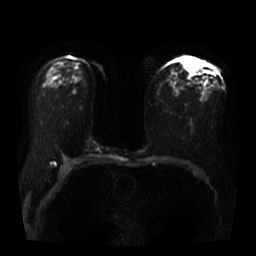
Breast MRI, one axial slice; slice 22 of 40 in the series (ordered by position); diffusion-weighted series; image 2 of 4 stored at this slice position (different b-values; order by instance number); 3 T; 5 mm slice thickness; 256 × 256 image matrix, field of view 360 × 360 mm. Female patient.
Outlined on this slice (expert manual segmentation):
- tumour on diffusion-weighted imaging: box from (x=183, y=58) to (x=197, y=75) px